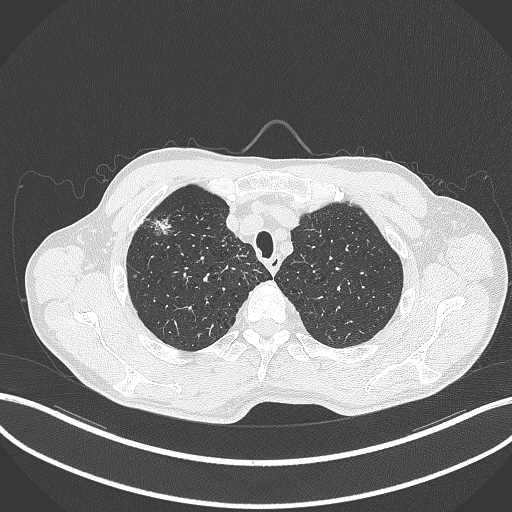
Chest CT, one axial slice; slice 354 of 427 in the series (ordered by position); 120 kVp; lung window (W 1500 / L -600 HU); 512 × 512 image matrix, field of view 400 × 400 mm. Male patient, age 69 years. Case-level facts recorded for this patient, not image findings: clinical TNM (as recorded): T1b N1 M0.
Outlined on this slice (bounding box drawn by a radiologist):
- lung tumour (recorded histology: adenocarcinoma): bounding box (x1, y1, x2, y2) in pixels: (148, 214, 176, 239)